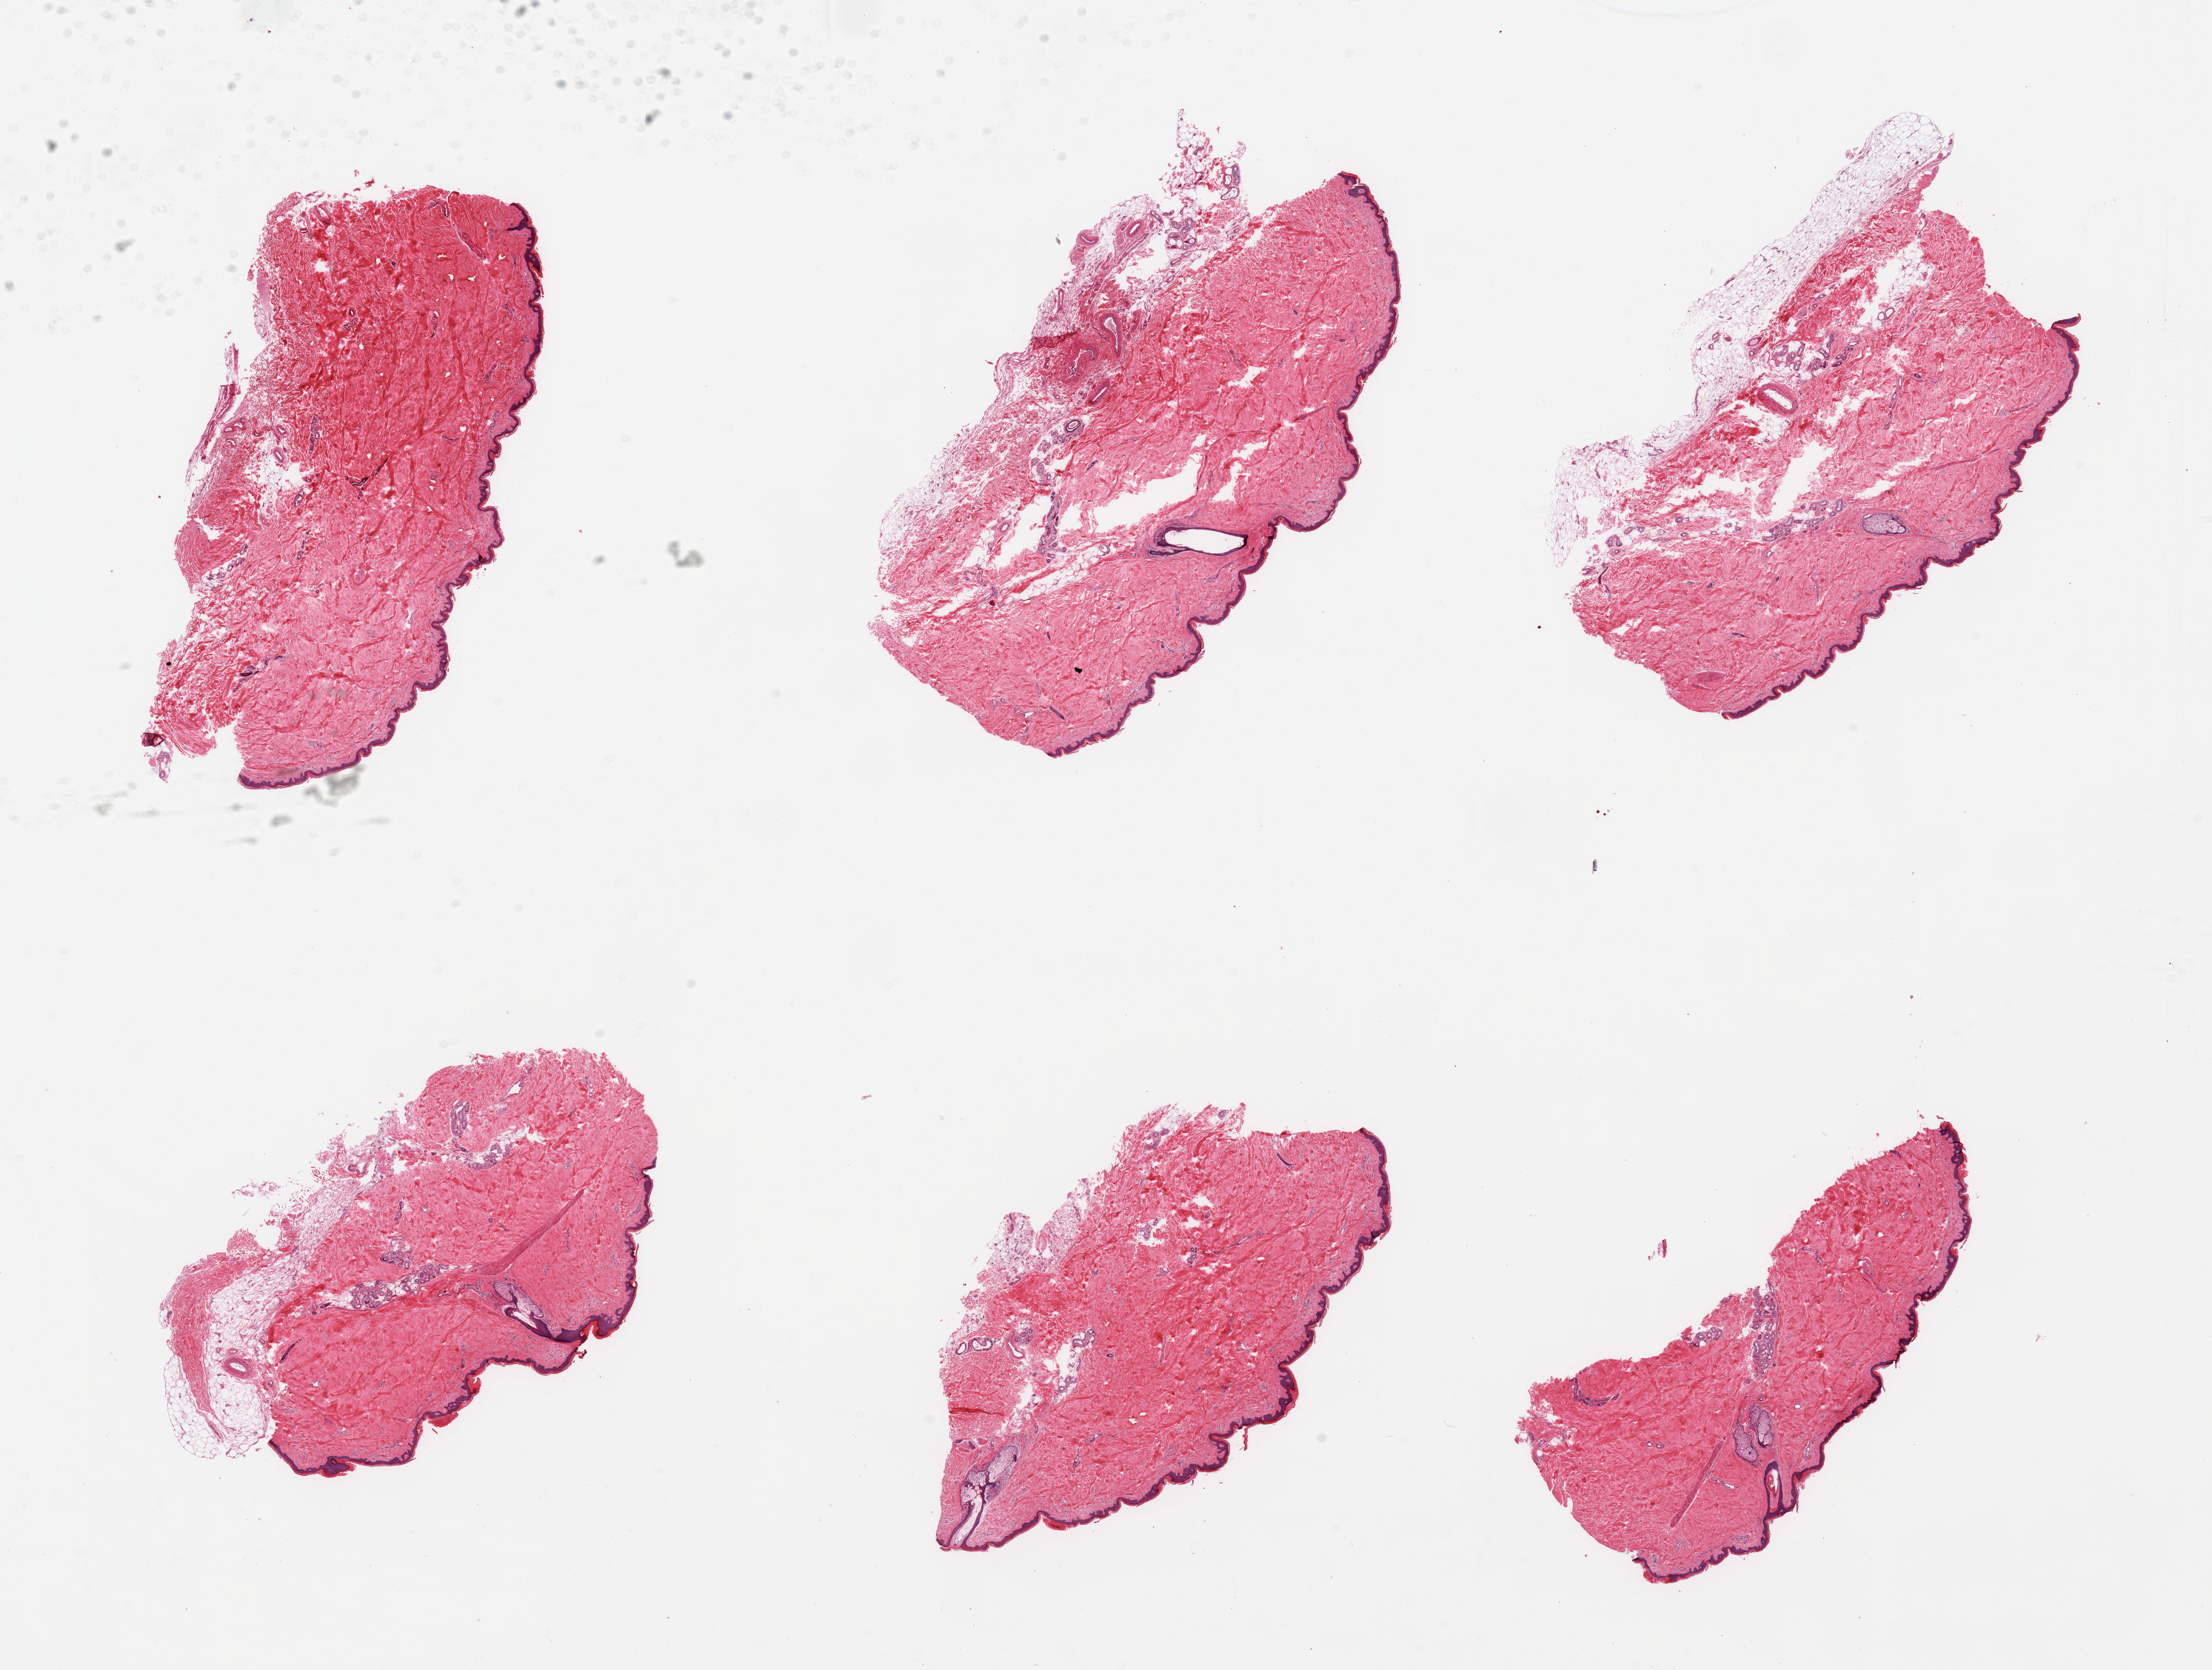
Digitized haematoxylin and eosin-stained section, low-resolution overview of the scanned area, about 23.6 x 17.8 mm. PAXgene-fixed paraffin-embedded (PFPE) section. Sampled site (target tissue): skin of lower leg. Tissue donor sample.
Review note (as recorded): 6 pieces; variable component of fat, mostly attached, up to 10%, epidermis measures 36 microns.